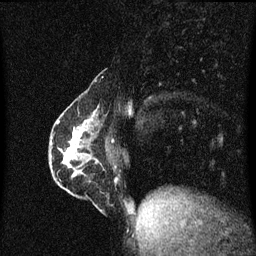
Breast MRI (dynamic contrast-enhanced), one sagittal slice; slice 21 of 60 in the series (ordered by position); dynamic contrast-enhanced series, image 2 of 3 at this slice position (ordered by acquisition); 1.5 T; TE 4.2 ms, TR 8.4 ms; 256 × 256 image matrix, field of view 200 × 200 mm. Female patient, age 40 years.
Structures marked on this image (semi-automatically segmented with operator editing):
- analysis volume of interest (the breast-tissue region the enhancement analysis was run in; not a lesion): box from (x=57, y=110) to (x=112, y=191) px
- tumour enhancement mask (voxels above the 70 % enhancement threshold inside the analysis volume of interest): (x=57, y=112)–(x=95, y=175)